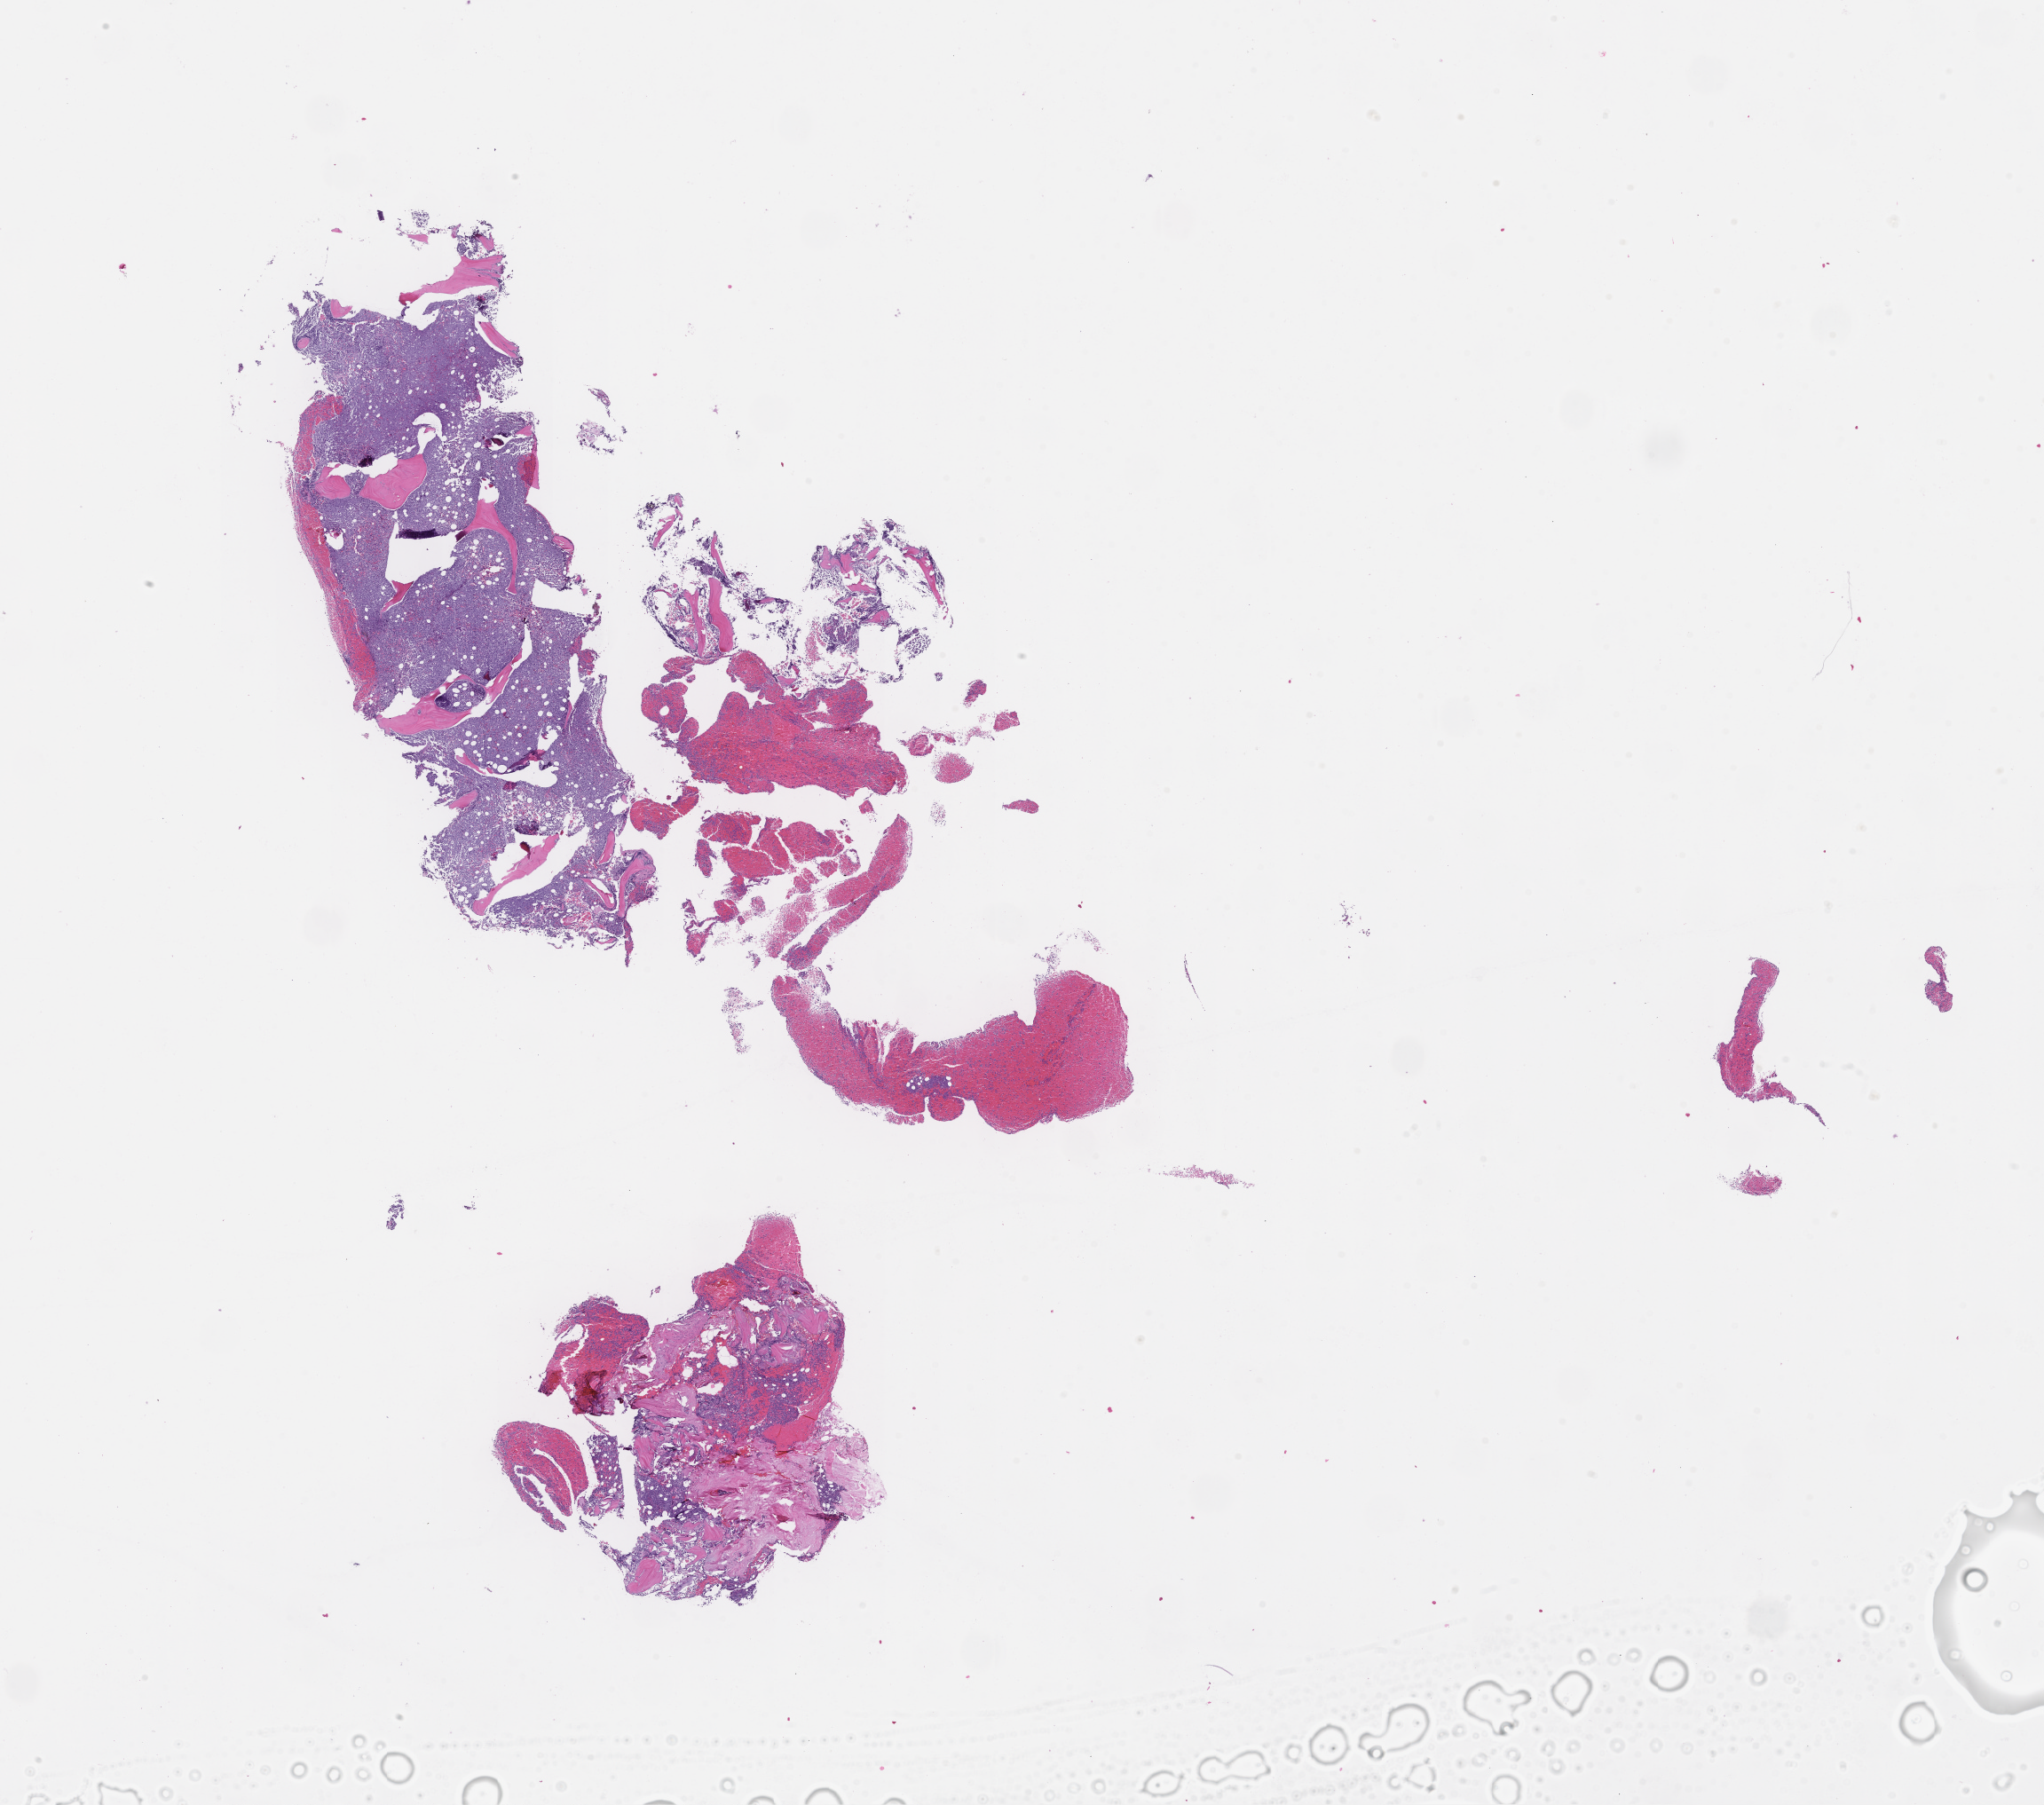
Whole-slide image, H&E stain — shown as a low-resolution overview of the whole scanned area (about 18.6 x 16.4 mm), formalin-fixed paraffin-embedded section, tissue site: bone marrow, specimen time point: collected at baseline (before treatment). Patient sex: female.
This section: primary tumor. Diagnosis: Acute Myeloid Leukemia Not Otherwise Specified.